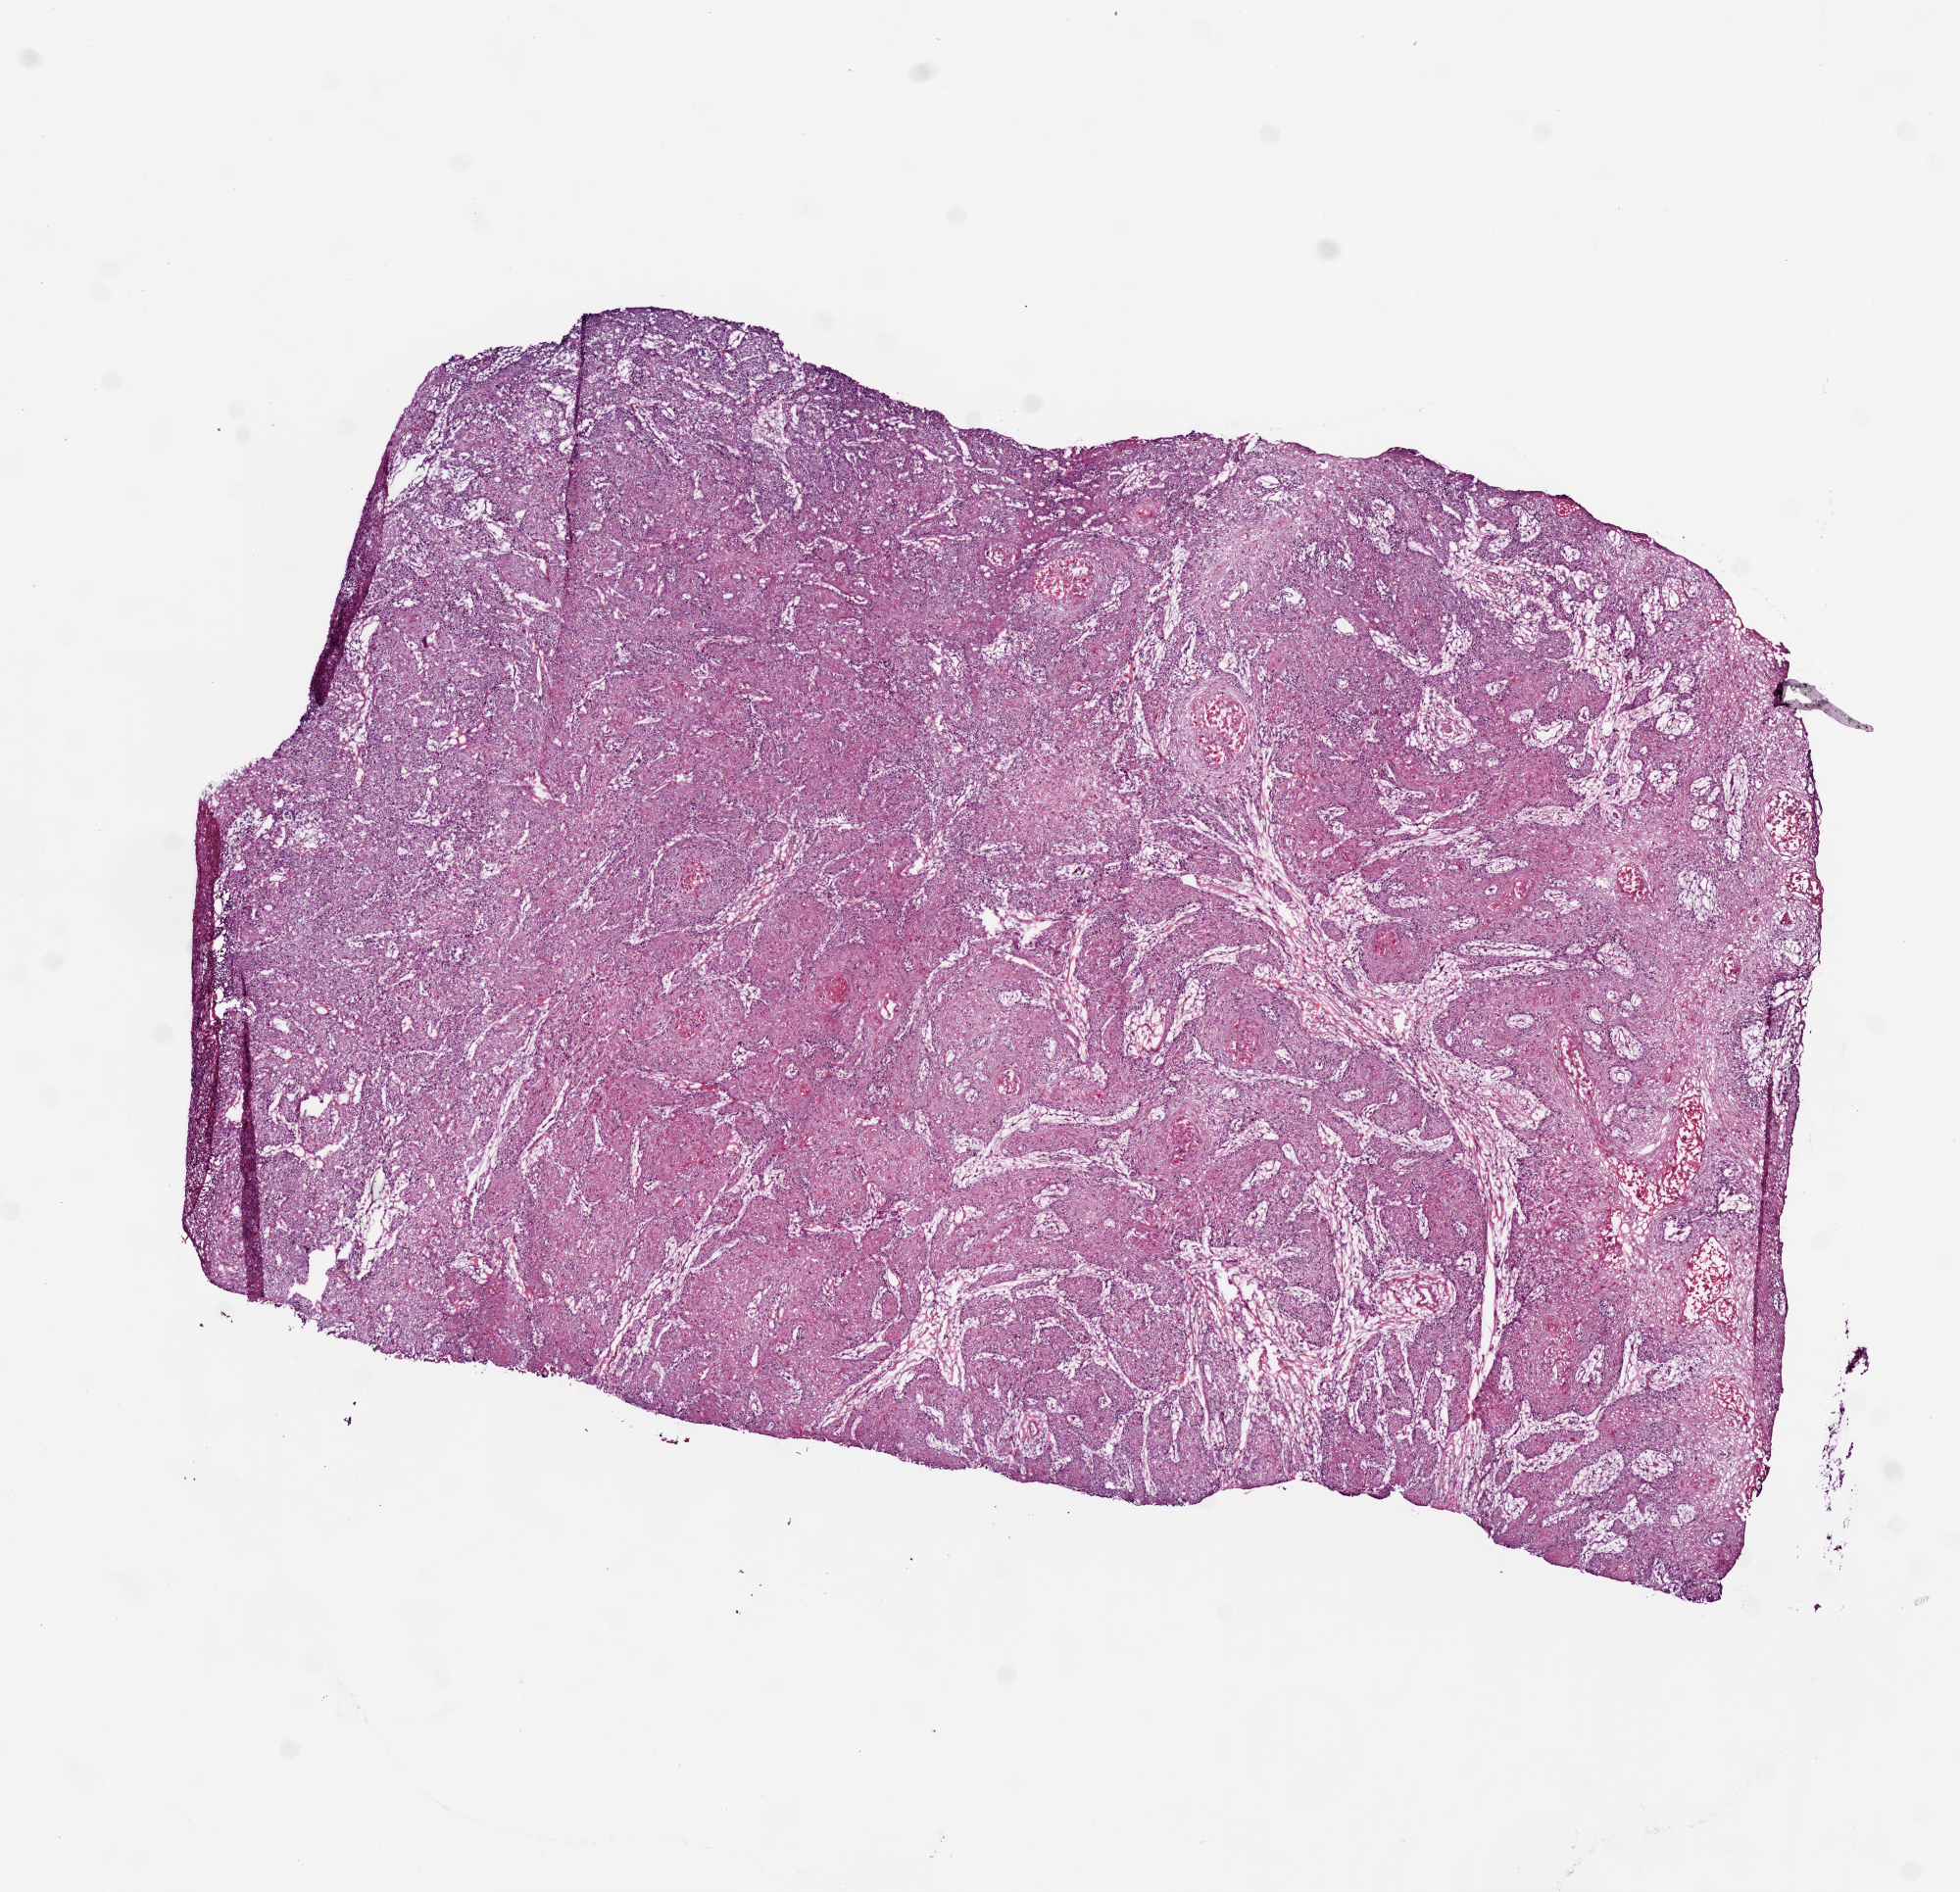
Whole-slide histology image, H&E, whole scanned area (about 8.0 x 7.7 mm, slide scanned at 20x) shown as a low-resolution overview; frozen section from the bottom of the tissue portion; primary tumour sample from the head and neck. Patient: male, age at initial diagnosis 70 years. Histologic grade: G2 (moderately differentiated). Pathologist review of this section (percent, as recorded): tumour cells 90%, tumour nuclei 85%, normal cells 0%, stromal cells 10%, necrosis 0%.
TNM: T2 N0. Diagnosis: Squamous cell carcinoma, NOS (cheek mucosa). AJCC pathologic stage: II.